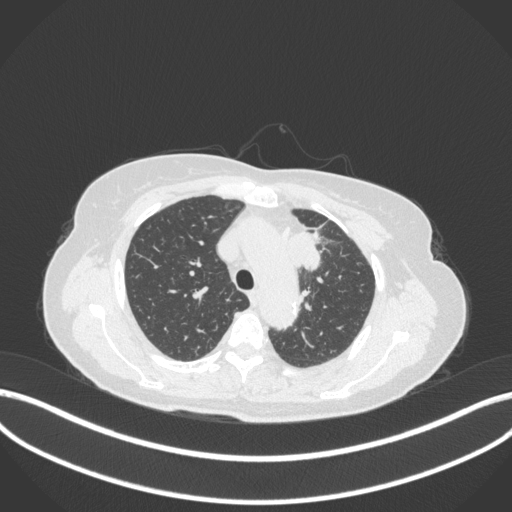
Chest CT, one axial slice; slice 248 of 368 in the series (ordered by position); reconstruction kernel B31f; lung window (W 1500 / L -600 HU); 1 mm slice thickness; 512 × 512 image matrix, field of view 400 × 400 mm. Female patient, age 65 years. Case-level facts recorded for this patient, not image findings: clinical TNM (as recorded): T2a N0 M0; histopathological grade: G2-3.
Annotated regions visible in this slice (bounding box drawn by a radiologist):
- lung tumour (recorded histology: adenocarcinoma): box from (x=287, y=228) to (x=323, y=273) px